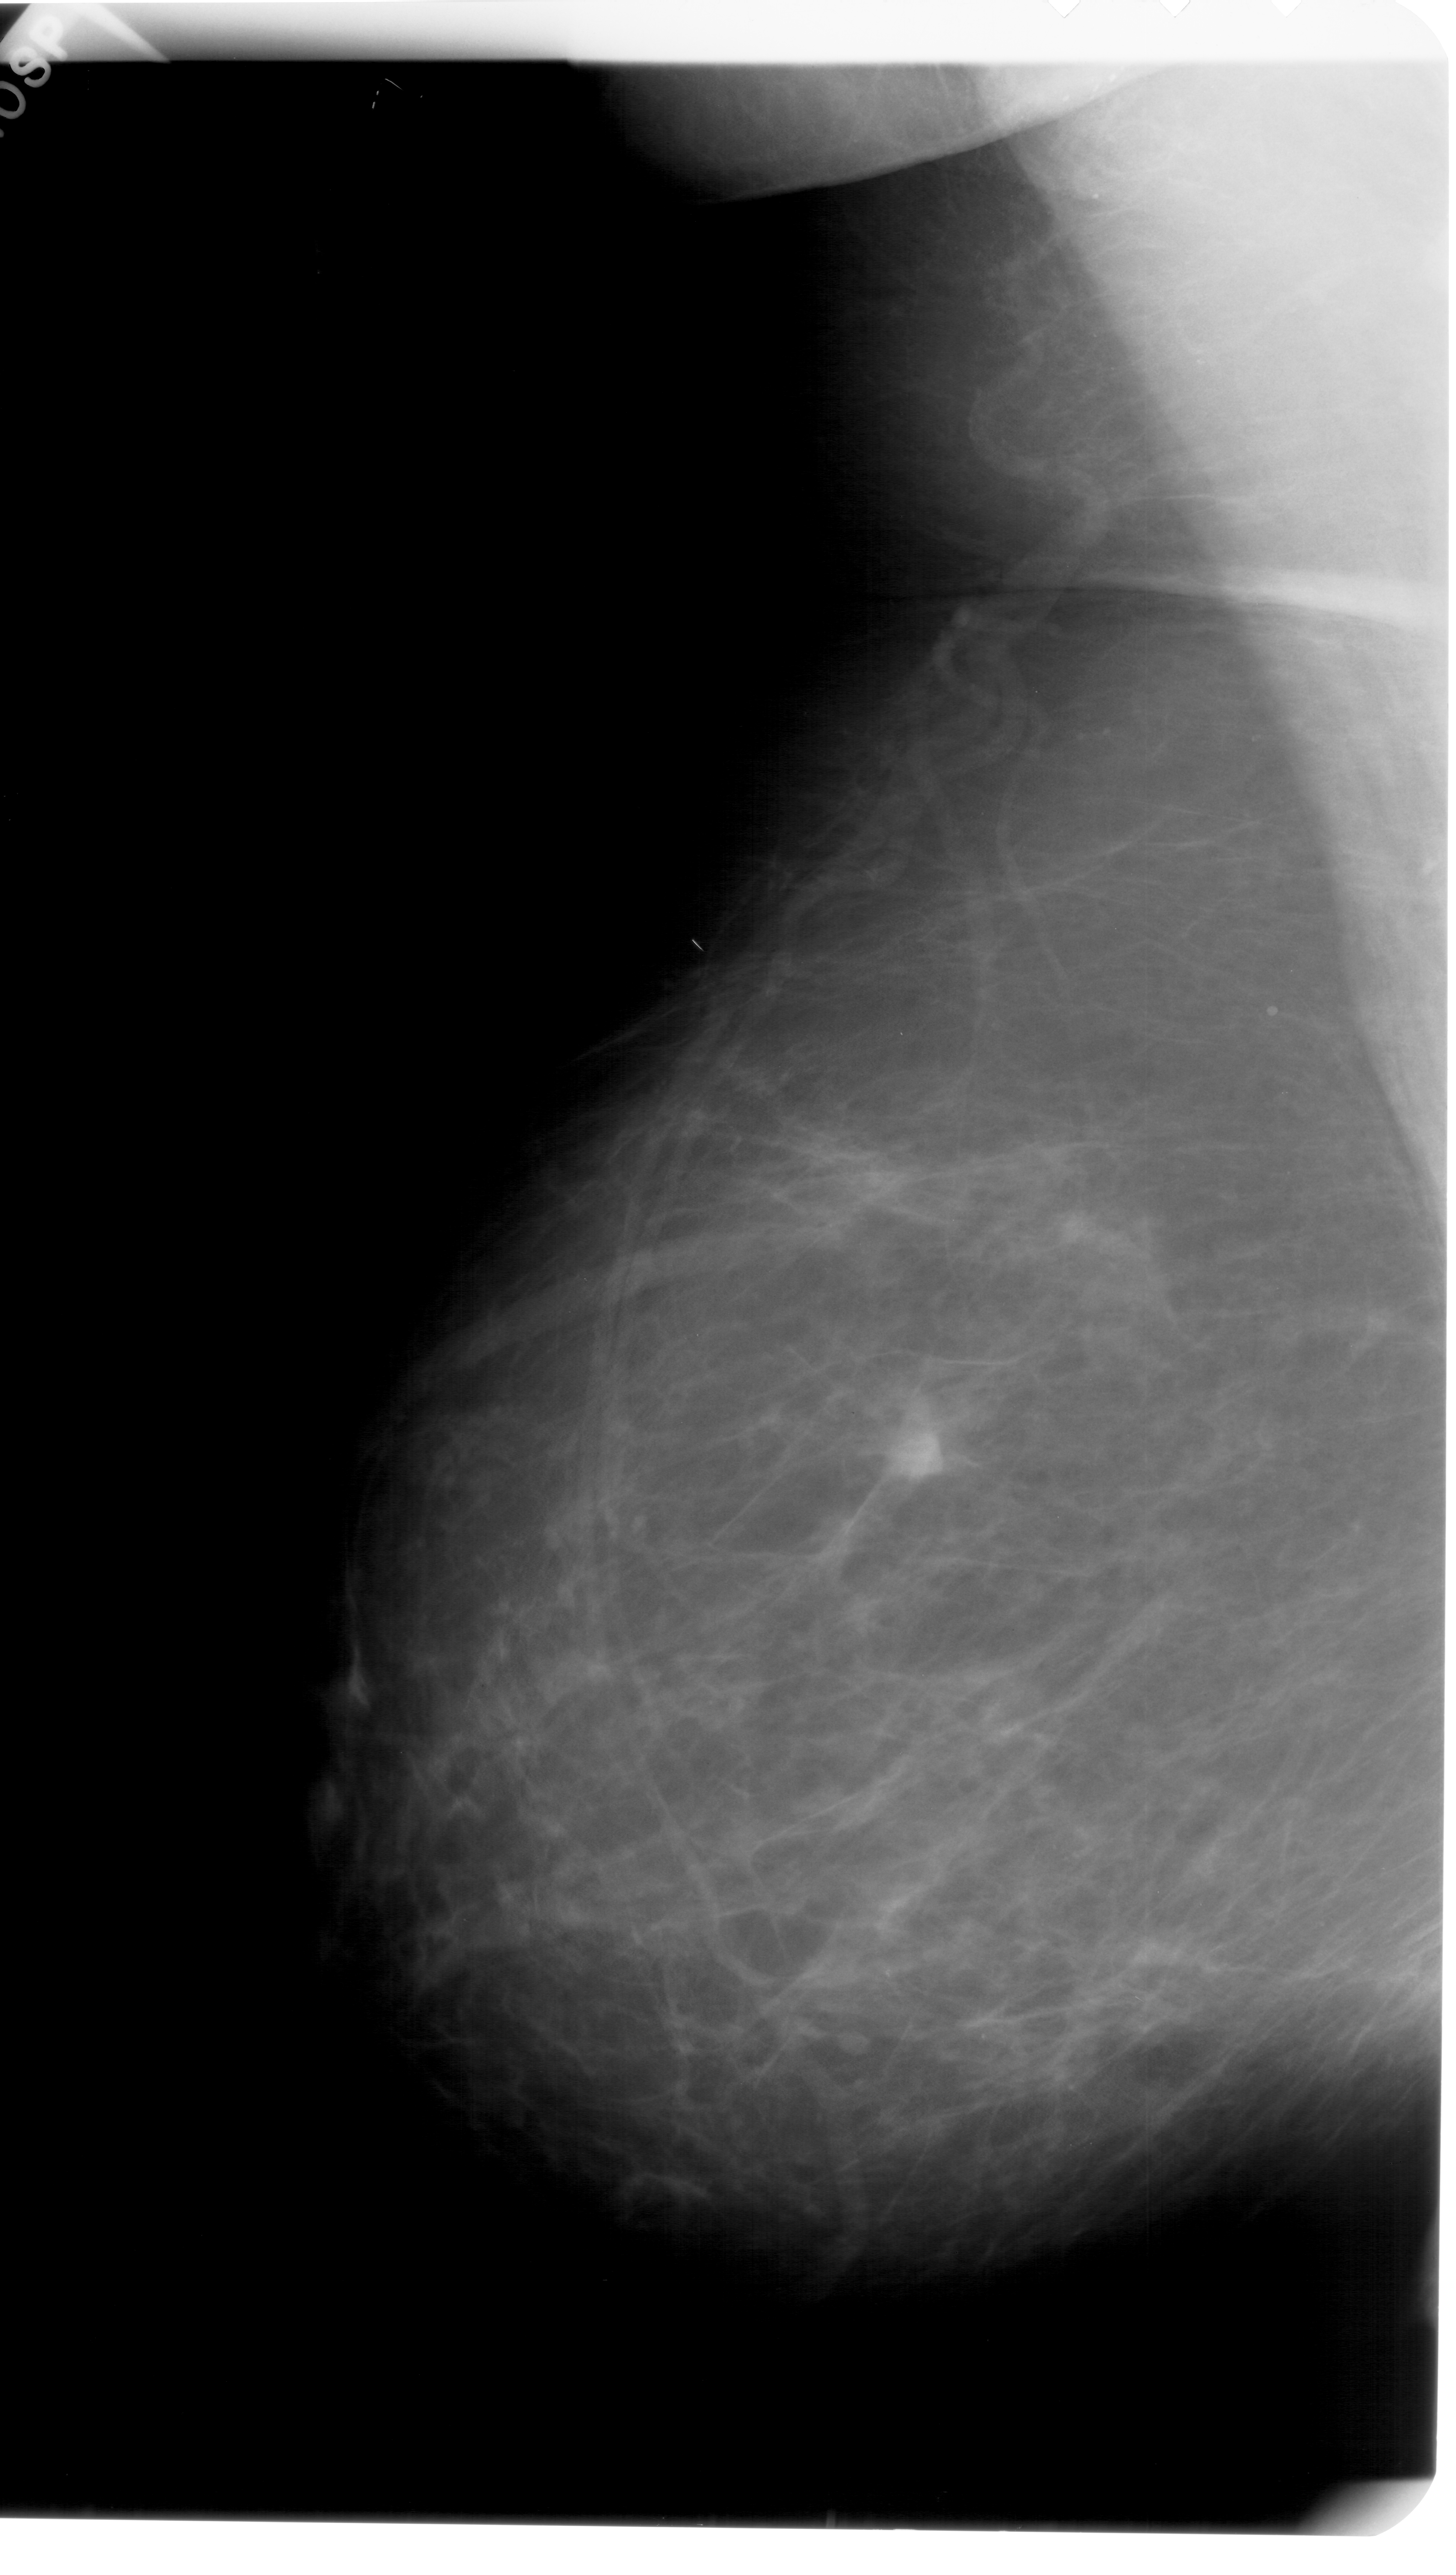
Mammogram (digitized film); left breast; MLO view; BI-RADS breast density category 2 (scale 1–4); 1456 × 2575 image matrix.
Expert-marked regions of interest on this image (one box per marked abnormality):
- mass, shape irregular, margins ill defined; BI-RADS assessment category 4; pathology result (as recorded, not read from the image): malignant: box from (x=854, y=1414) to (x=953, y=1507) px